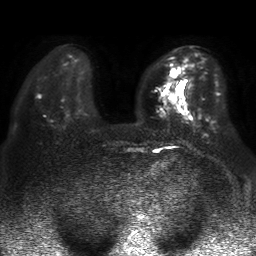
Breast MRI, one axial slice; slice 14 of 50 in the series (ordered by position); diffusion-weighted series; image 2 of 4 stored at this slice position (different b-values; order by instance number); 1.5 T; 256 × 256 image matrix, field of view 360 × 360 mm. Female patient.
Structures marked on this image (outlined manually by an expert reader):
- tumour on diffusion-weighted imaging: bounding box [x1, y1, x2, y2] px = [169, 69, 180, 103]